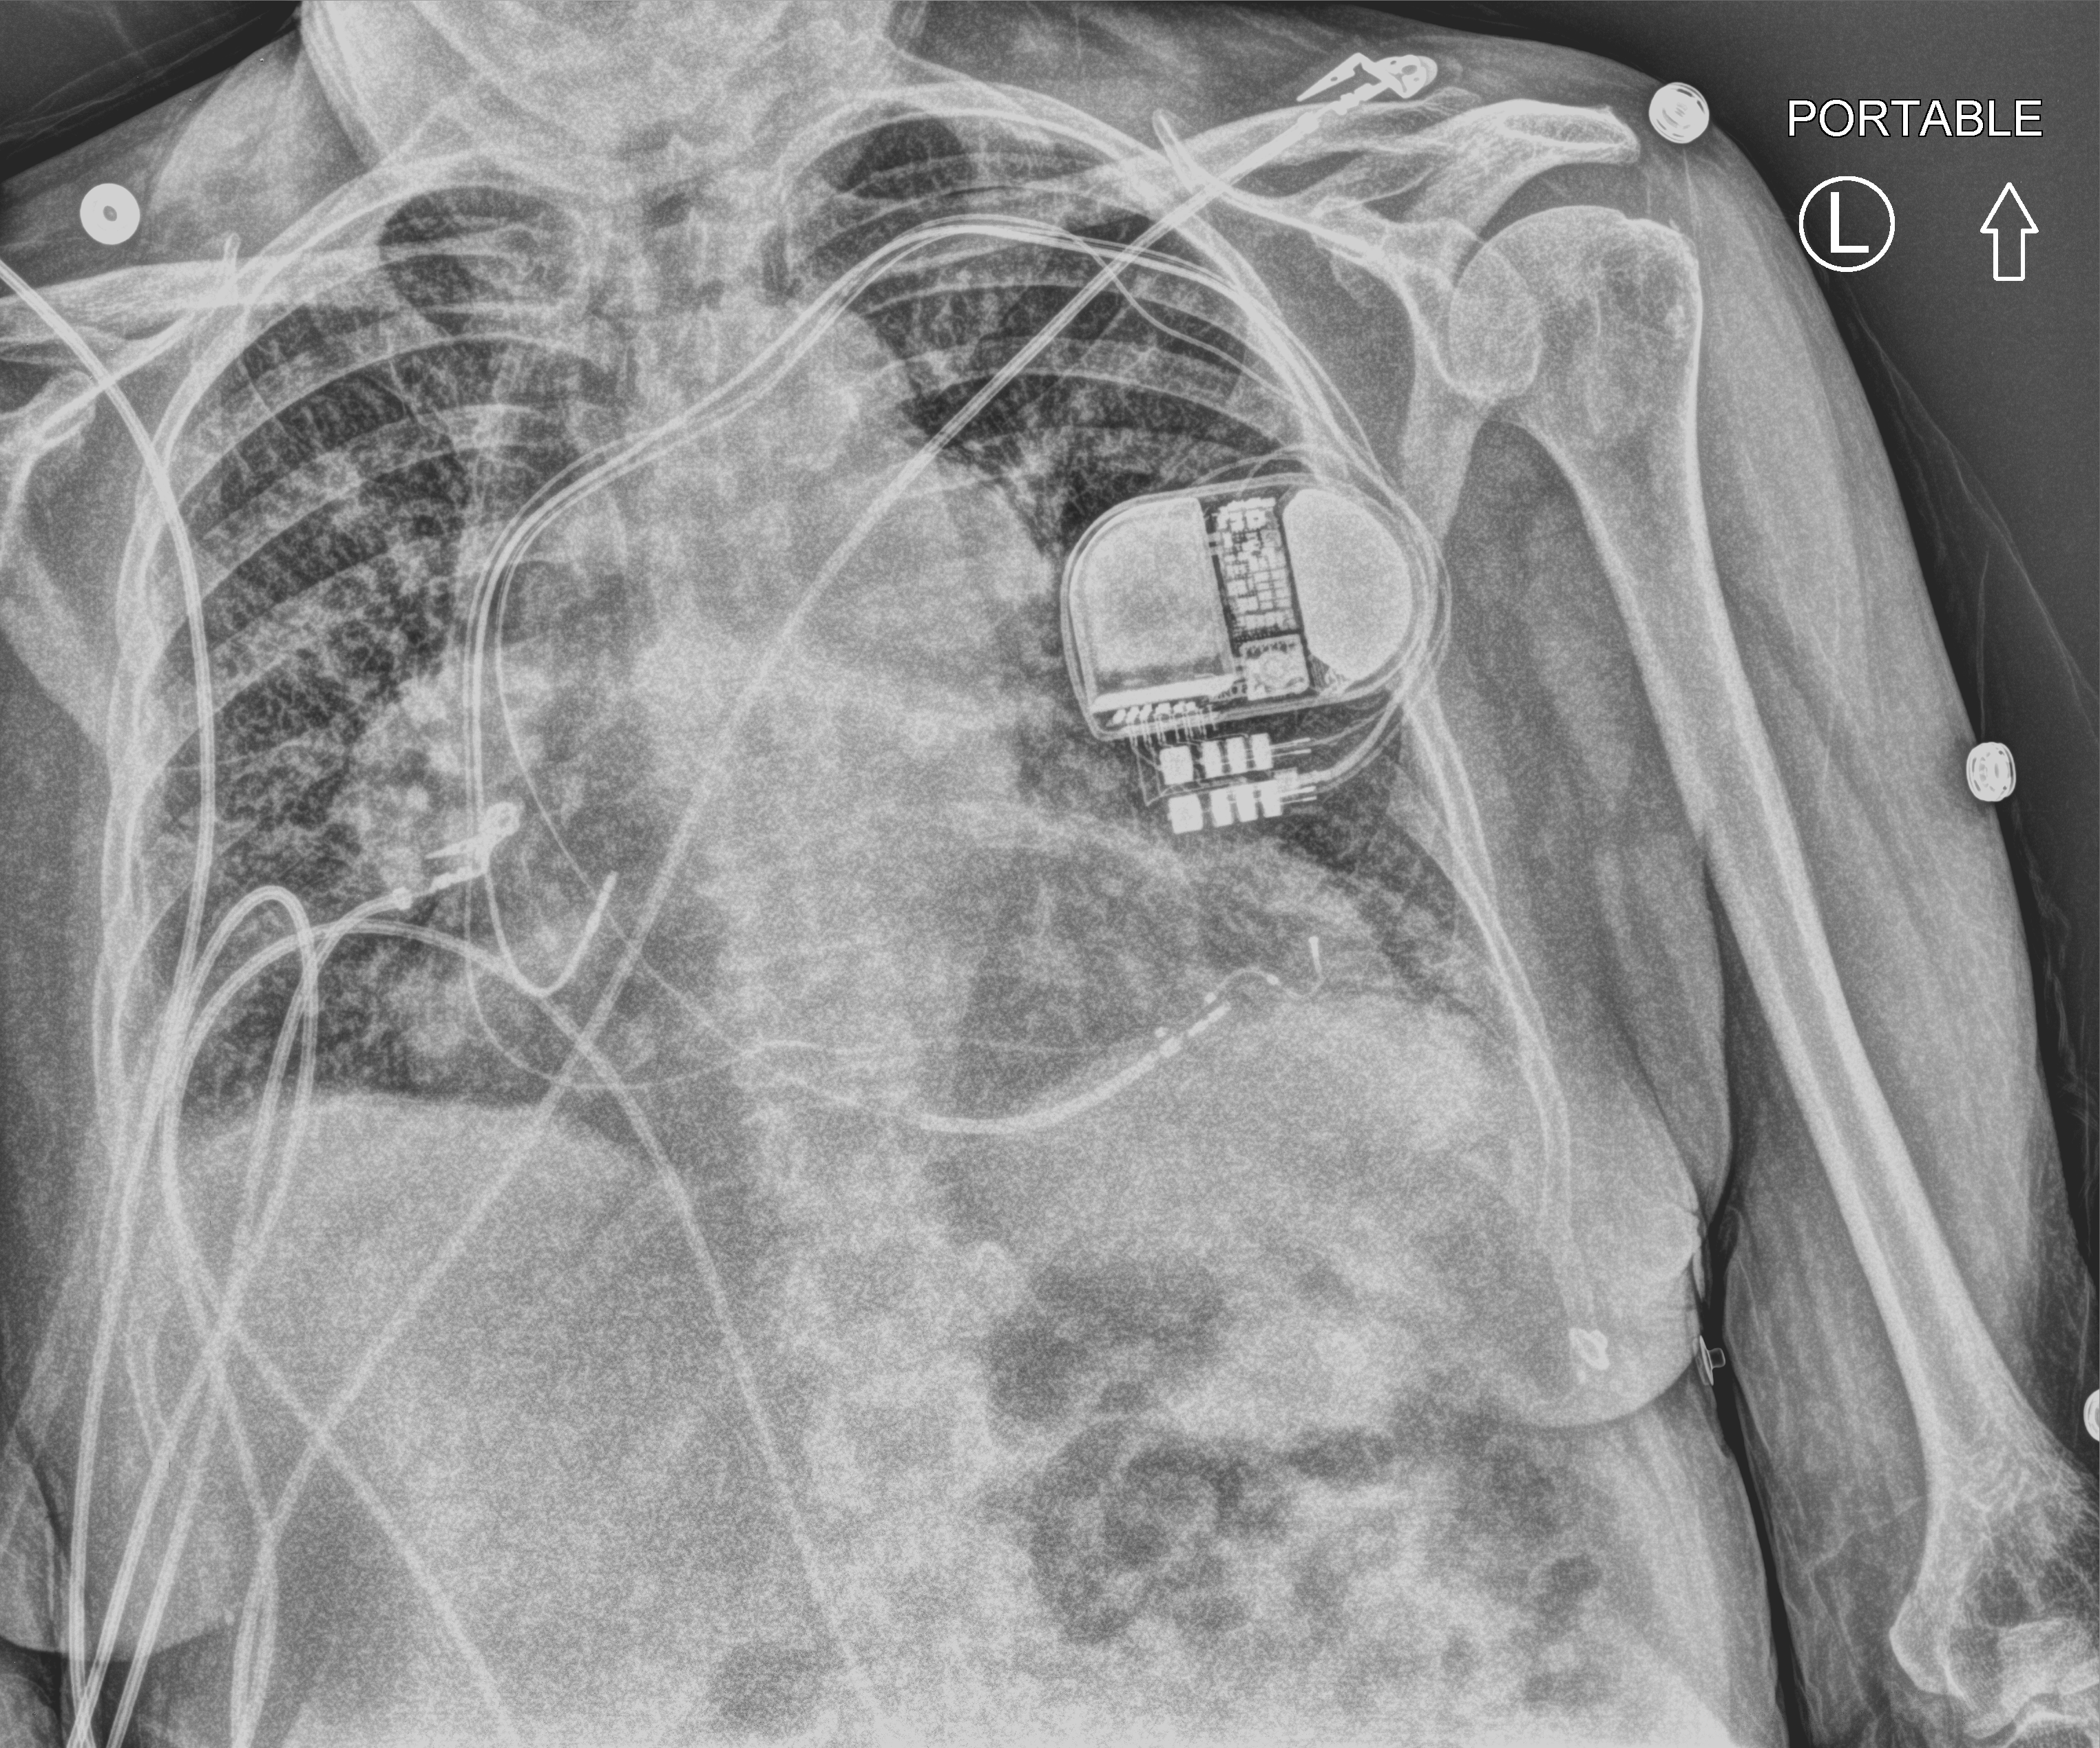
Portable chest radiograph; anteroposterior (AP) projection. Female patient hospitalised with COVID-19, age 60–74 years.
Hospital-stay facts (about this admission, not read from this image; timing relative to this image not recorded): admitted to intensive care during this hospital stay: yes.